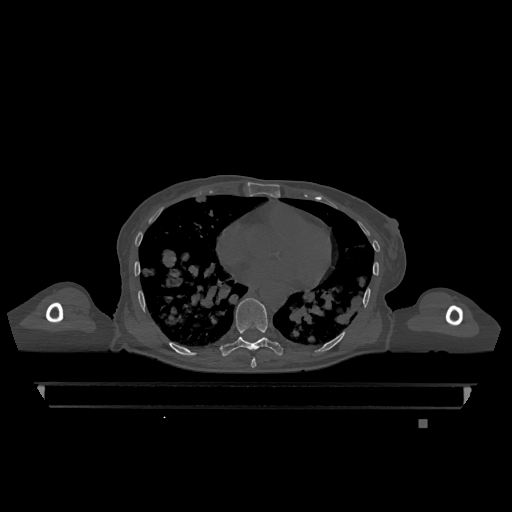
CT including the spine, one axial slice. Position 693 of 1317 along the scan axis. Bone window (W 1800 / L 400 HU). 0.5 mm slice thickness. 512 × 512 image matrix, field of view 500 × 500 mm. Patient: female, 74 years. From the clinical record (not read from this slice): primary cancer: lung; vertebrae with lytic lesions (as recorded): T1, T4, T5, T6, L4, L5.
Outlined on this slice (semi-automatically segmented with operator editing):
- T7 vertebra: bounding box (x1, y1, x2, y2) in pixels: (251, 357, 257, 368)
- T9 vertebra: (220, 298, 283, 357)